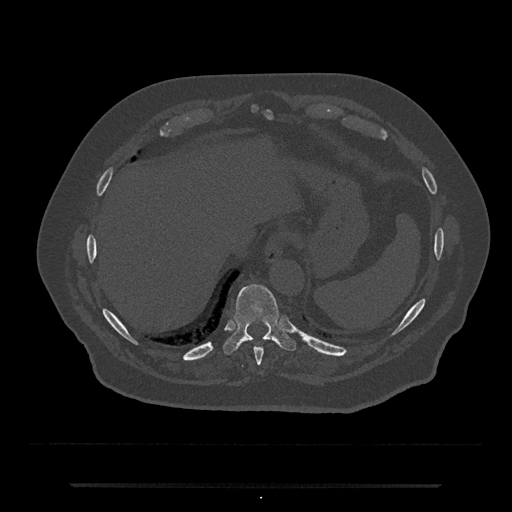
CT including the spine, one axial slice. Slice 722 of 797 in the series (ordered by position). 120 kVp. Bone window (W 1800 / L 400 HU). 0.5 mm slice thickness. 512 × 512 image matrix, field of view 434 × 434 mm. Patient: male, 80 years. From the clinical record (not read from this slice): primary cancer: prostate.
Structures marked on this image (semi-automatically segmented with operator editing):
- T10 vertebra: bounding box <222,284,296,355> (left, top, right, bottom; pixels)
- T9 vertebra: <254,347,264,366>